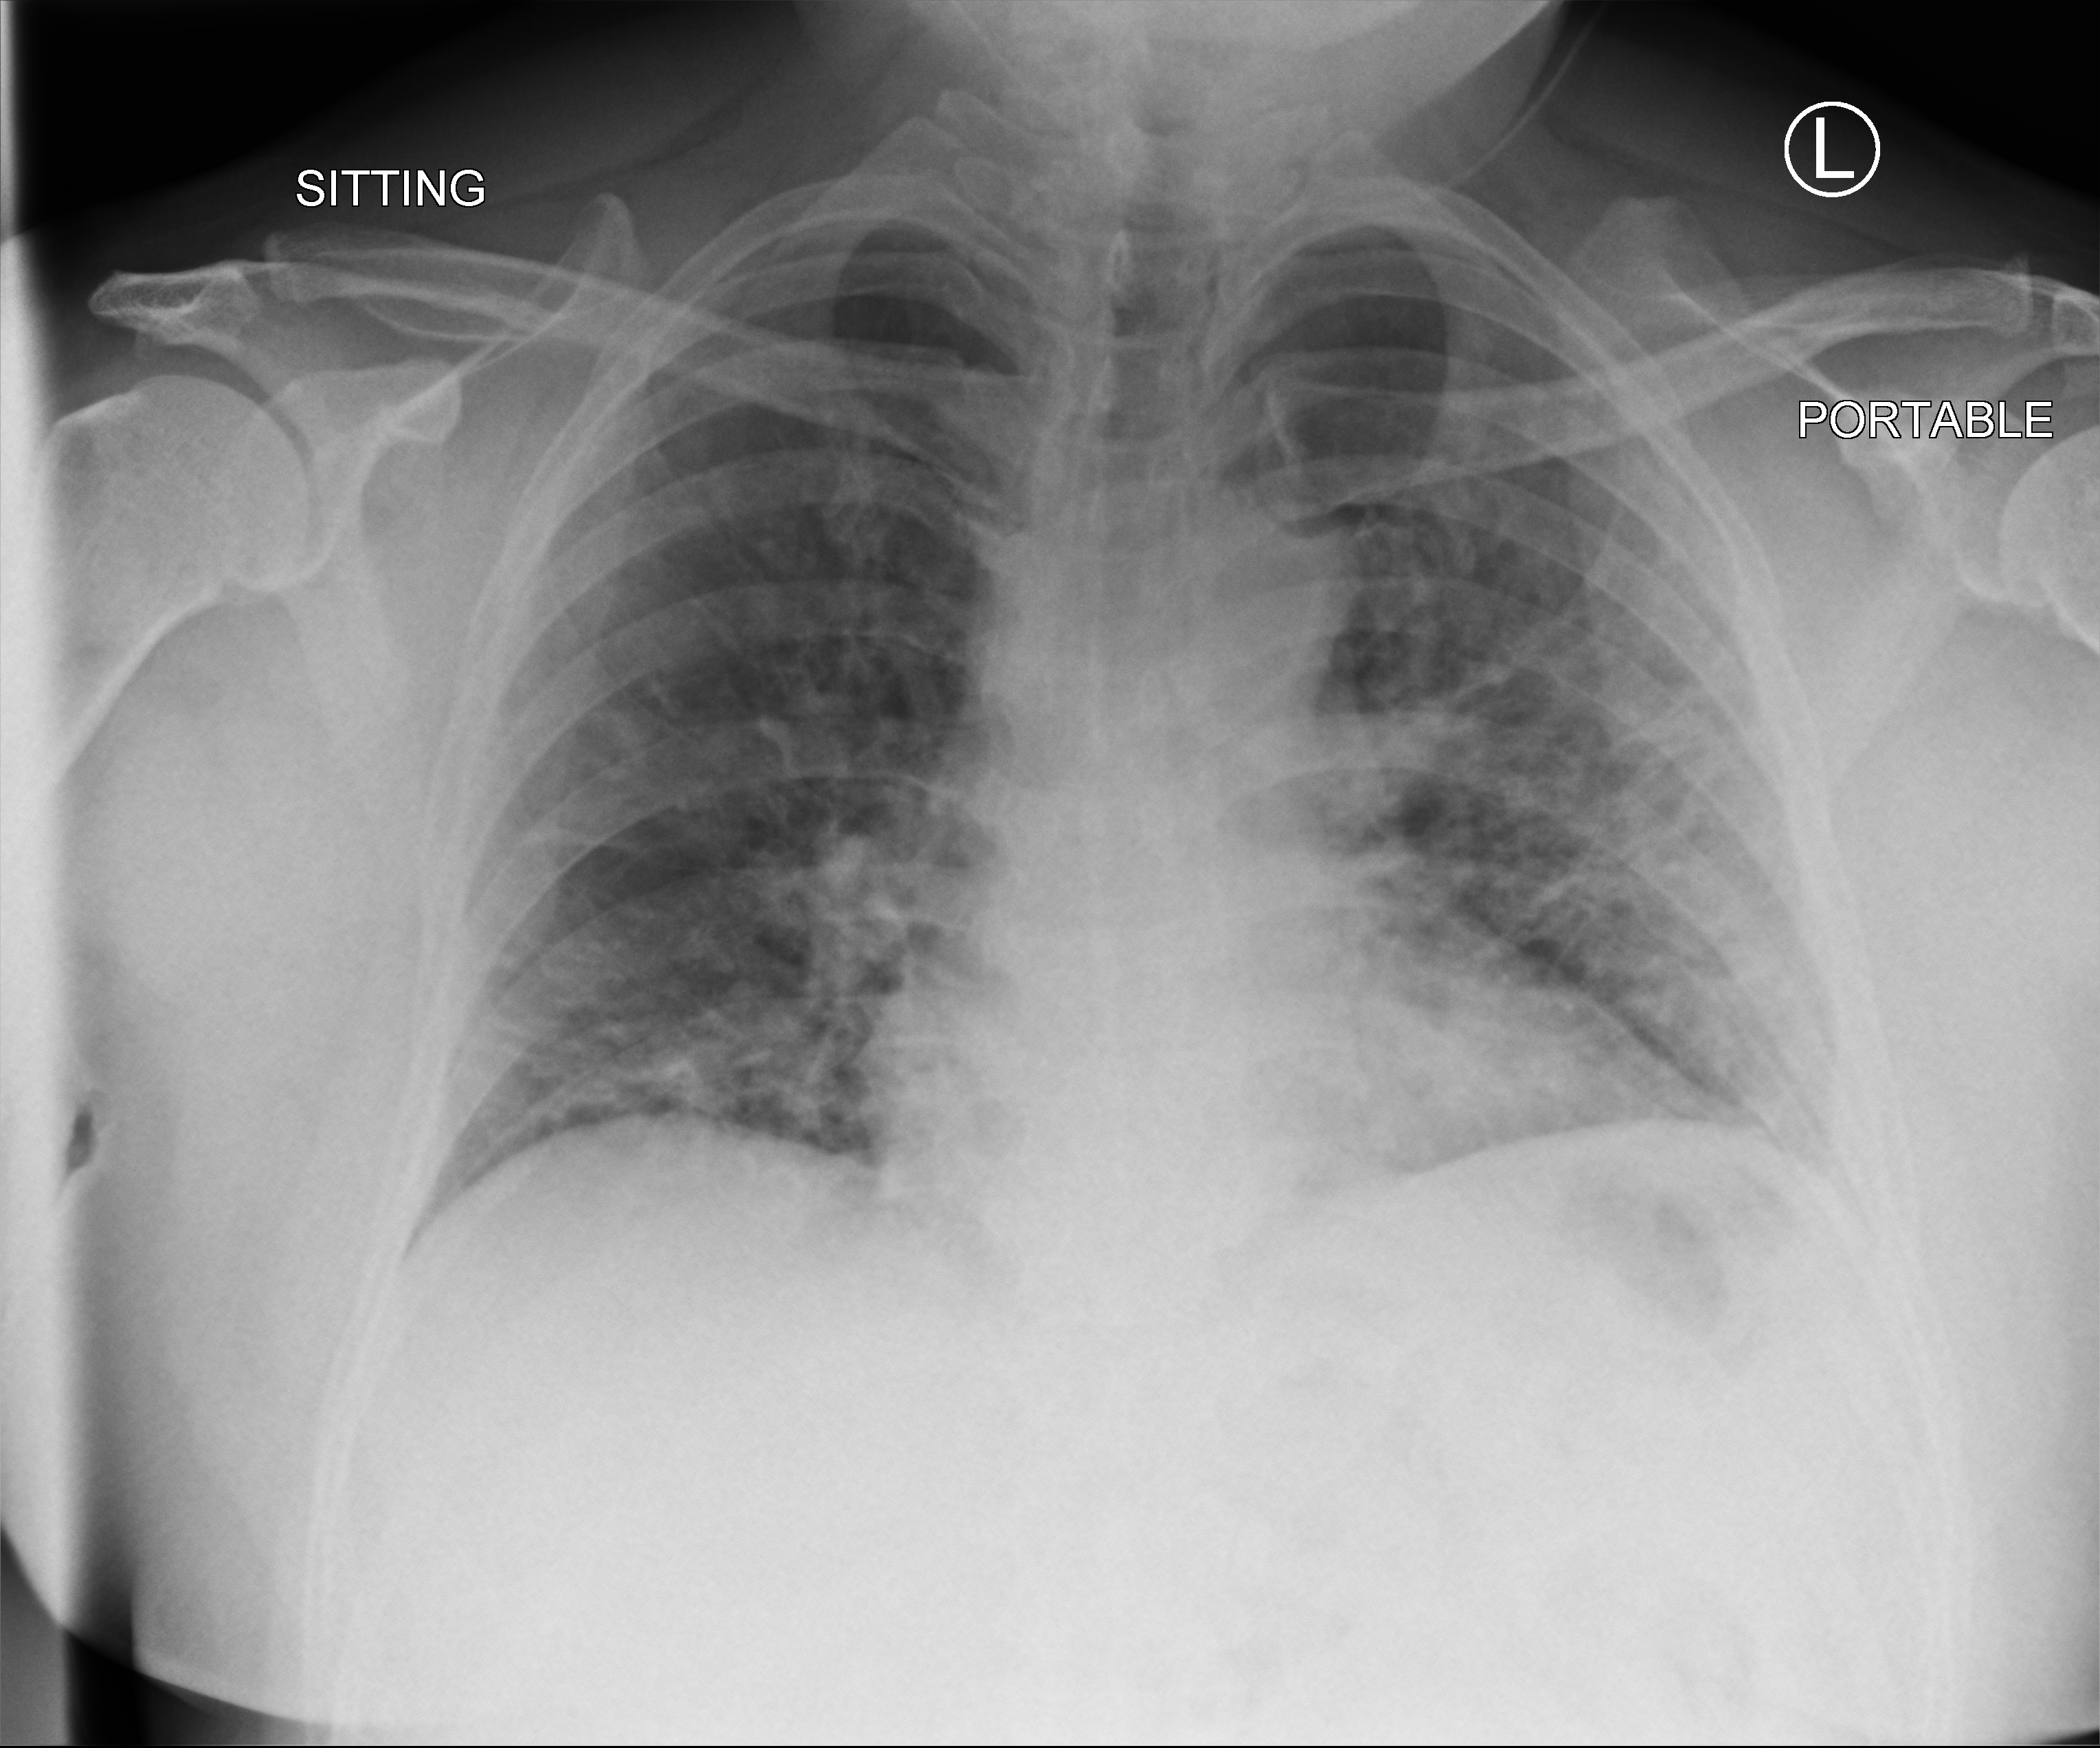
Bedside chest radiograph (computed radiography); anteroposterior (AP) projection. Male patient hospitalised with COVID-19, age 18–59 years.
From the hospital-stay record, not from the radiograph (when in the stay this image was taken is not recorded): admitted to intensive care during this hospital stay: yes.